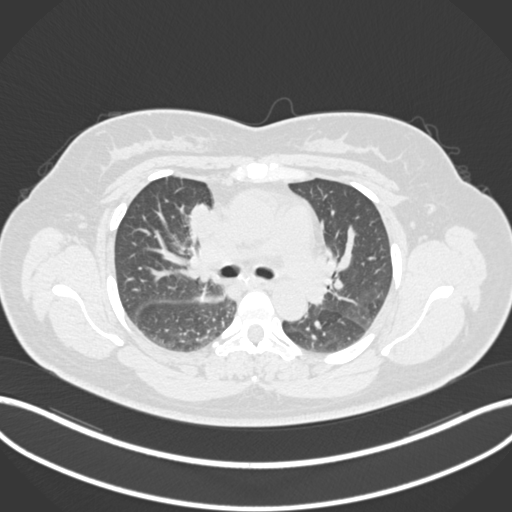
Chest CT, one axial slice. Lung window (W 1500 / L -600 HU). 1 mm slice thickness. 512 × 512 image matrix, field of view 400 × 400 mm. Patient: female, 46 years. Case-level facts recorded for this patient, not image findings: clinical TNM (as recorded): T2a N1 M0.
Structures marked on this image (rectangle marked by the reading radiologist):
- lung tumour (recorded histology: adenocarcinoma): bounding box (x1, y1, x2, y2) in pixels: (187, 201, 223, 242)